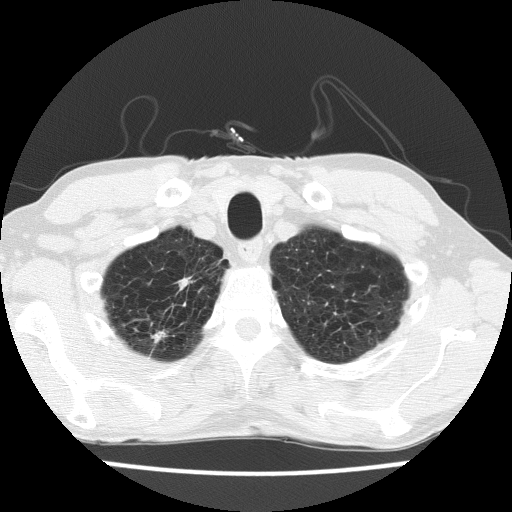
Low-dose screening chest CT, axial slice, second screening round (one year after baseline), lung window (W 1500 / L -600 HU), lung (sharp) reconstruction kernel (FC51), slice 20 of 175 in the series. Male, age 63 years at enrolment. Current smoker at enrolment.
Expert reader's lesion annotation, bounding box <136,262,204,332> (left, top, right, bottom; pixels). Screening reader's record for this exam: no non-calcified nodule ≥4 mm recorded. Official screen result: negative screen, minor abnormalities not suspicious for lung cancer. Lung cancer was diagnosed 390 days after this screen (after the third annual screen): adenocarcinoma, NOS, right upper lobe, moderately differentiated (G2), stage IIIB (AJCC 6th edition), 17 mm at pathology.